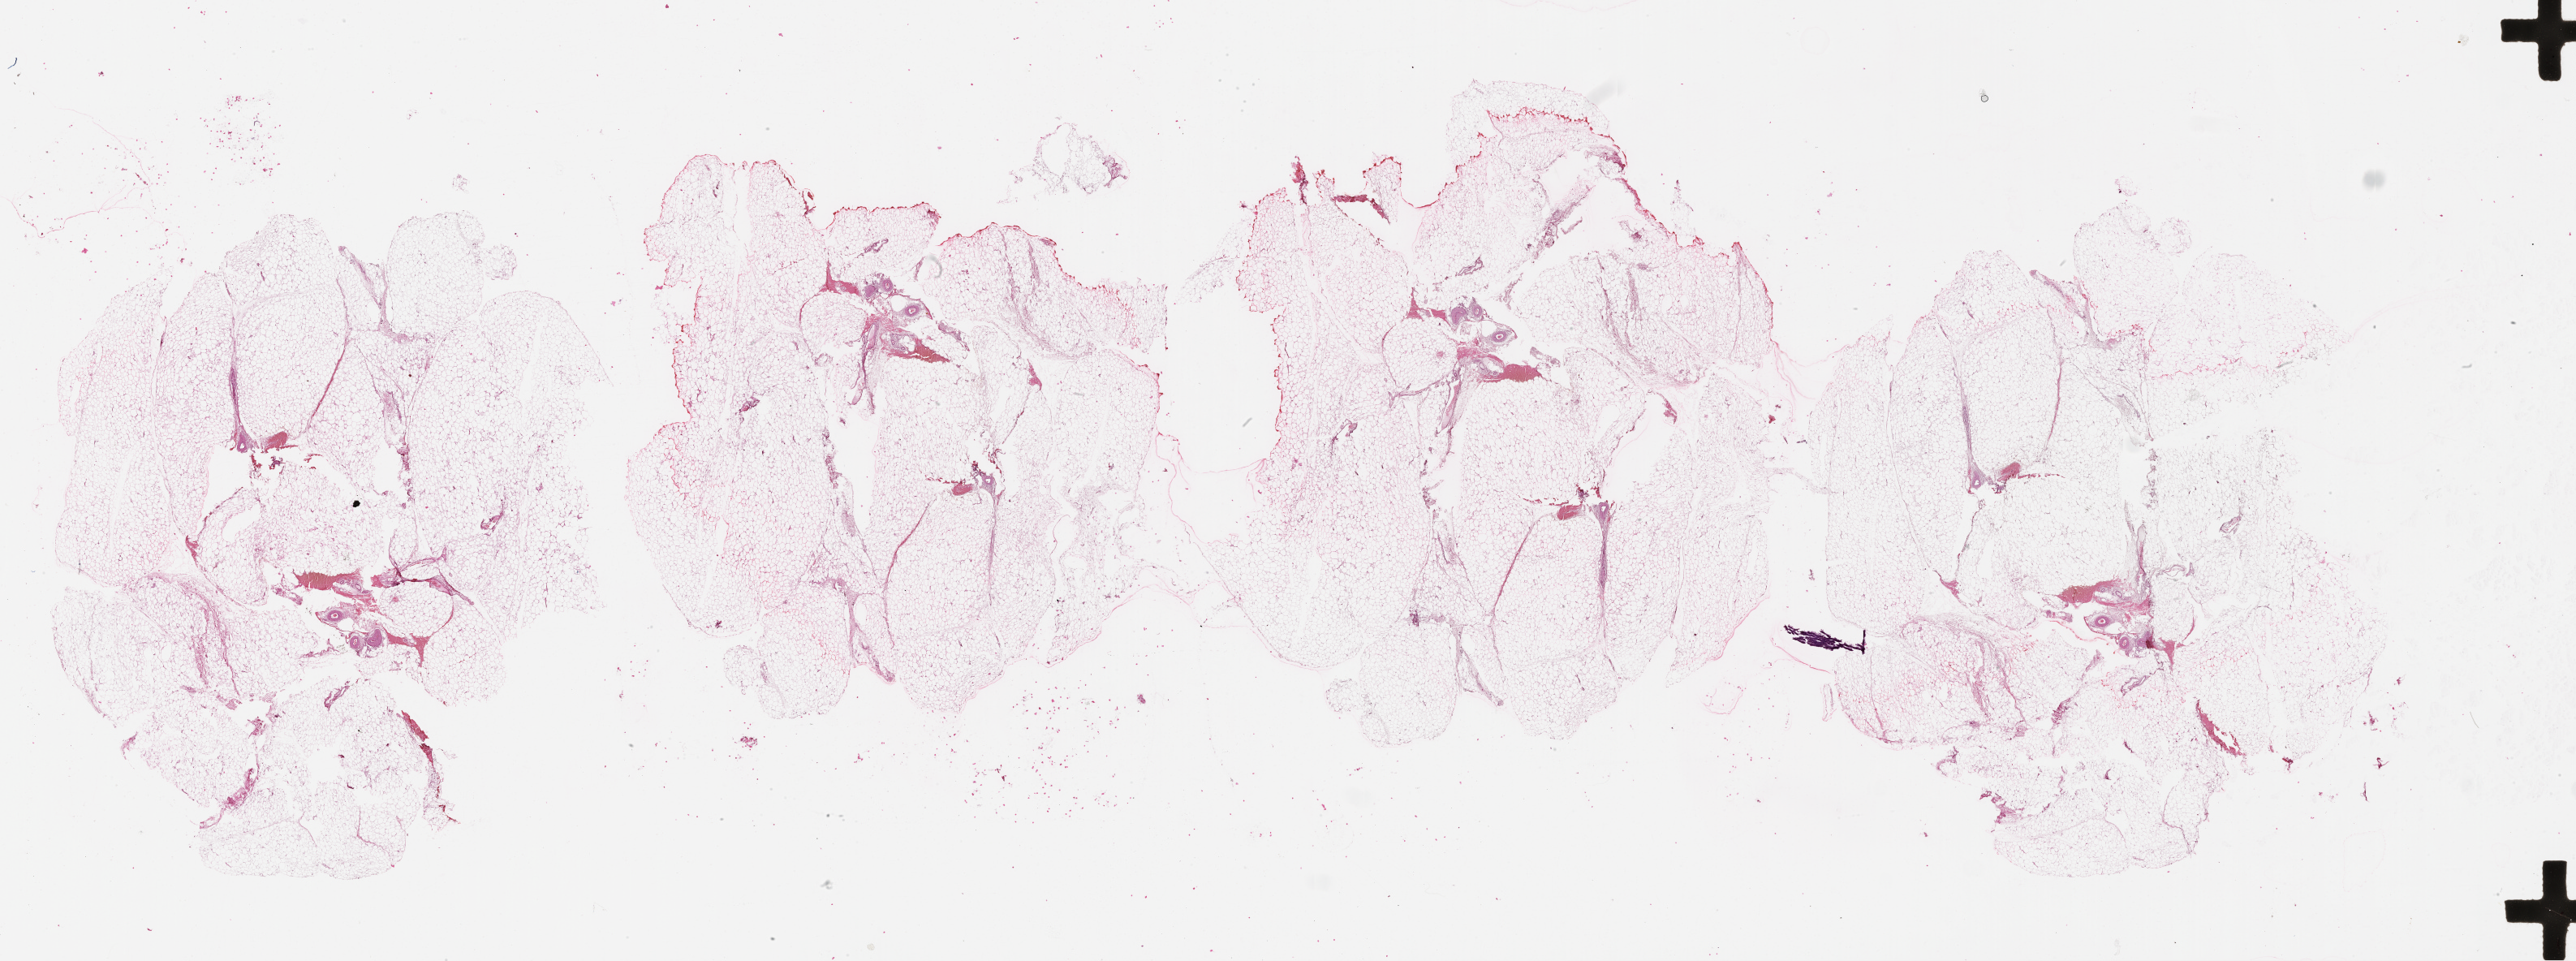
Whole-slide histology image, H&E — low-resolution overview of the scanned area, about 51.1 x 19.1 mm. Female, 76 y/o.
* patient diagnosis: Malignant melanoma, NOS